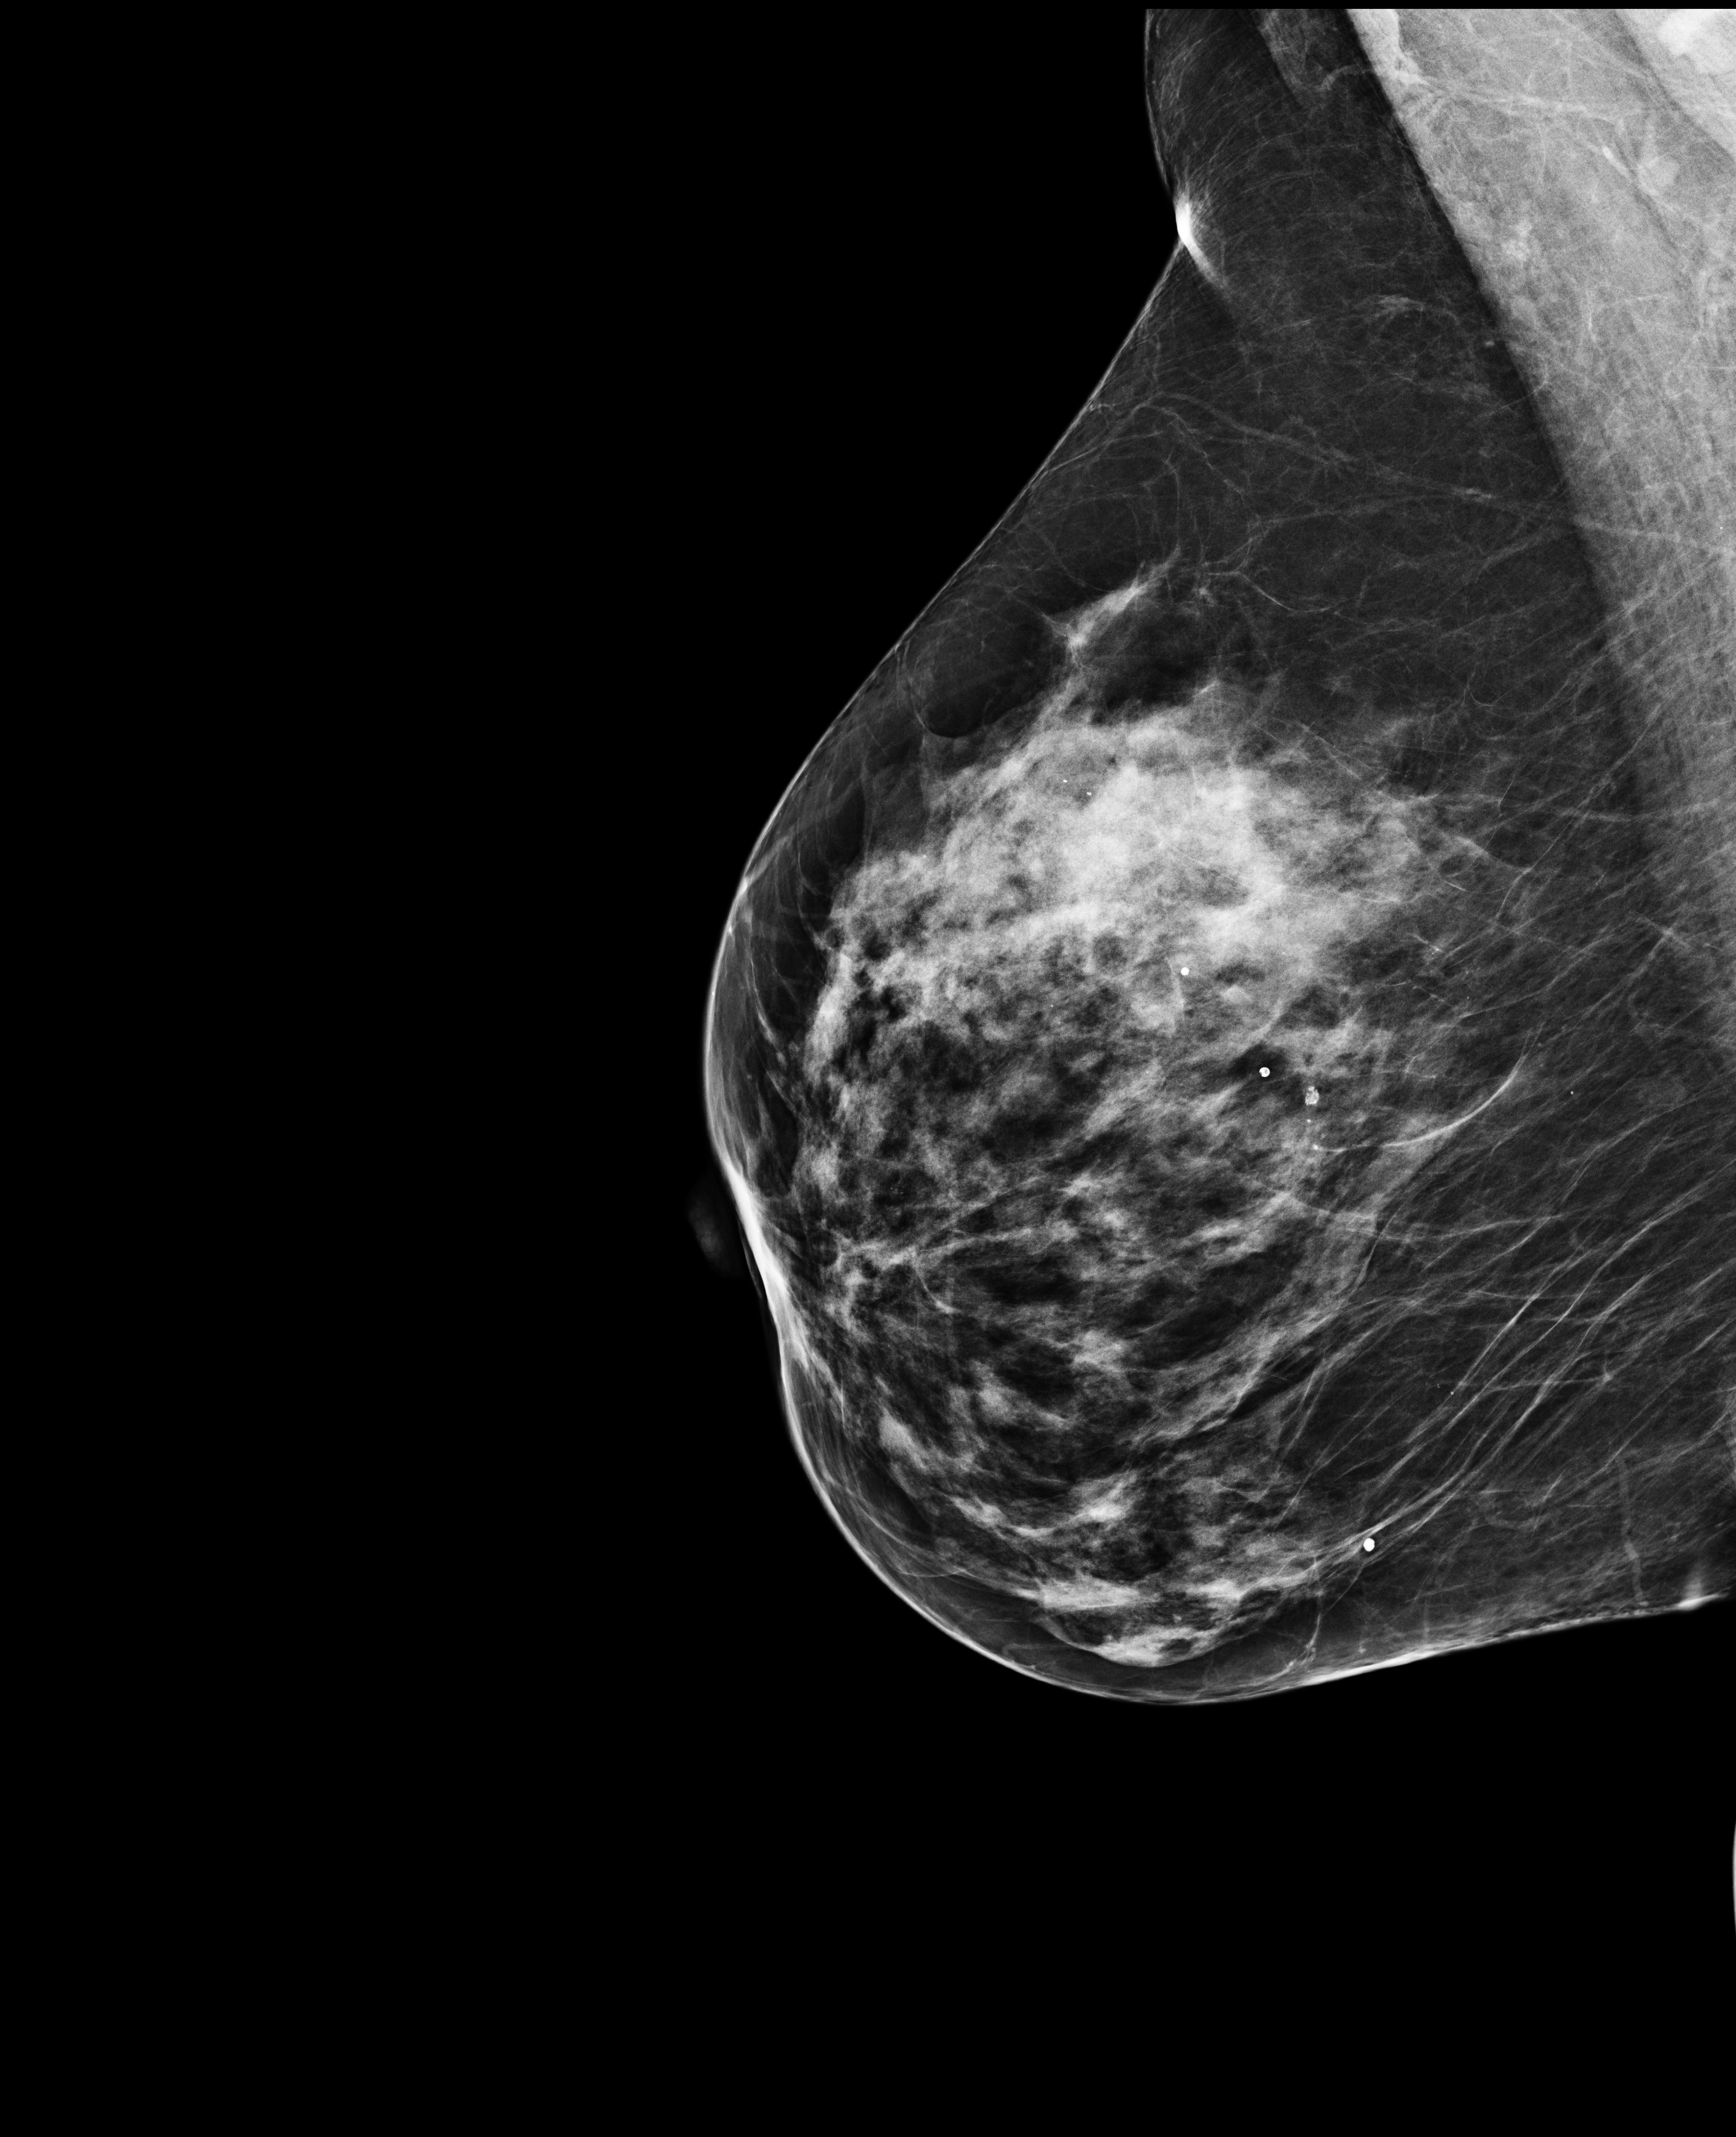
Full-field digital mammogram (FFDM); right breast; mediolateral oblique (MLO) view; screening examination. Patient aged 62 years (female).
Breast density at the screening exam (both breasts): heterogeneously dense (BI-RADS density category c). Final BI-RADS category for the screening round (tomosynthesis exam, both breasts): category 2. Recall: no recall after this screen.